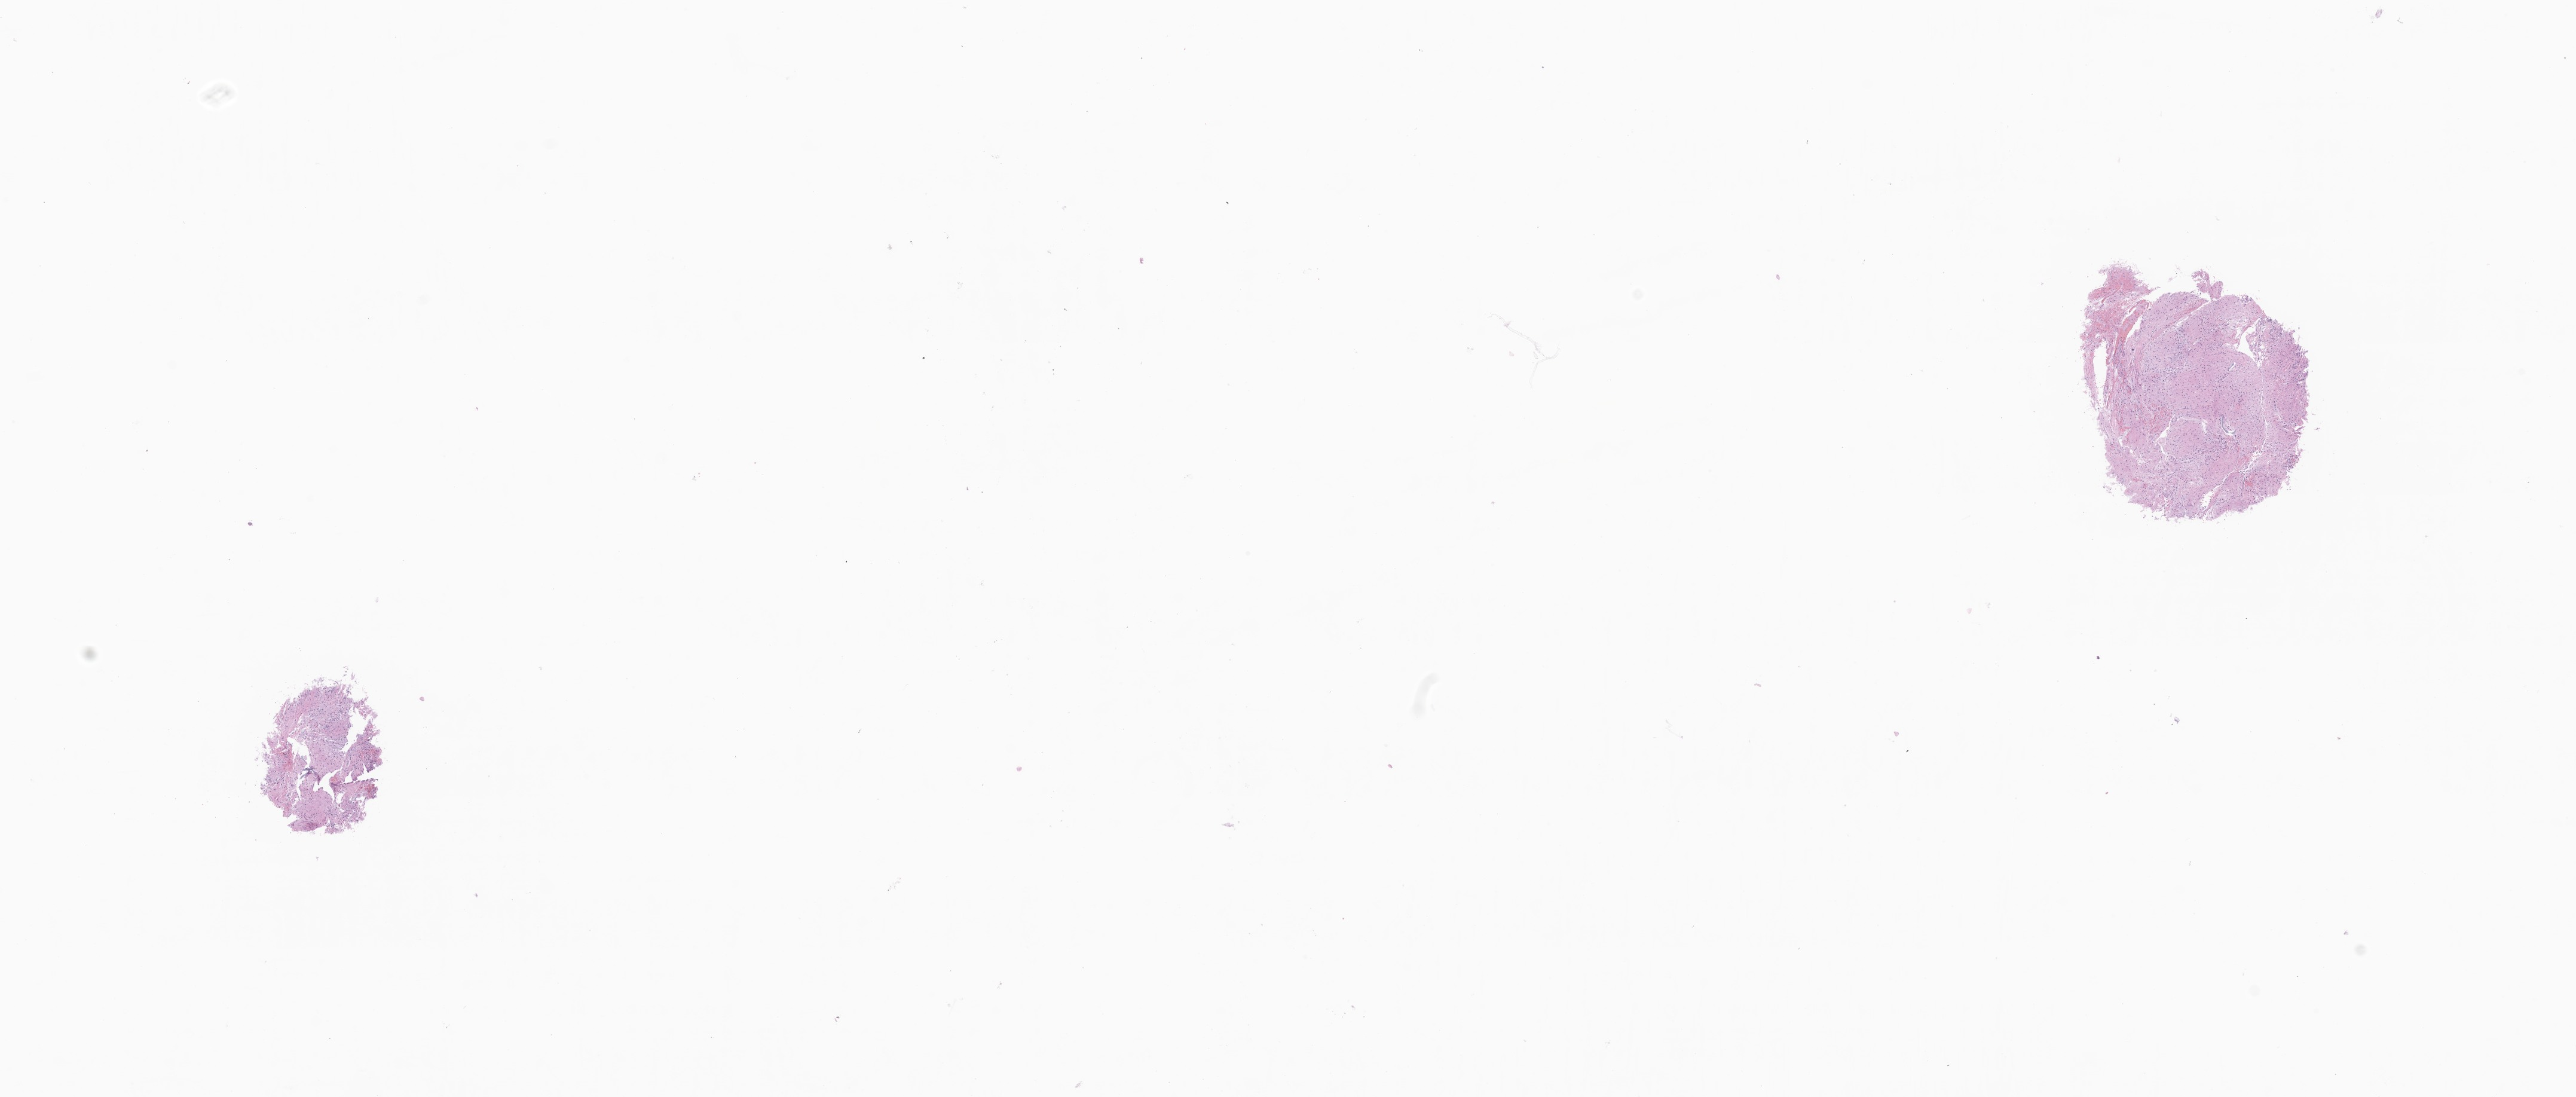
Hematoxylin and eosin (H&E) whole-slide image of tumor tissue from the brain — whole scanned area (about 18.2 x 7.7 mm) shown as a low-resolution overview, formalin-fixed paraffin-embedded section. Patient: male, age 192 months.
Recorded diagnosis: Neoplasm, uncertain whether benign or malignant.